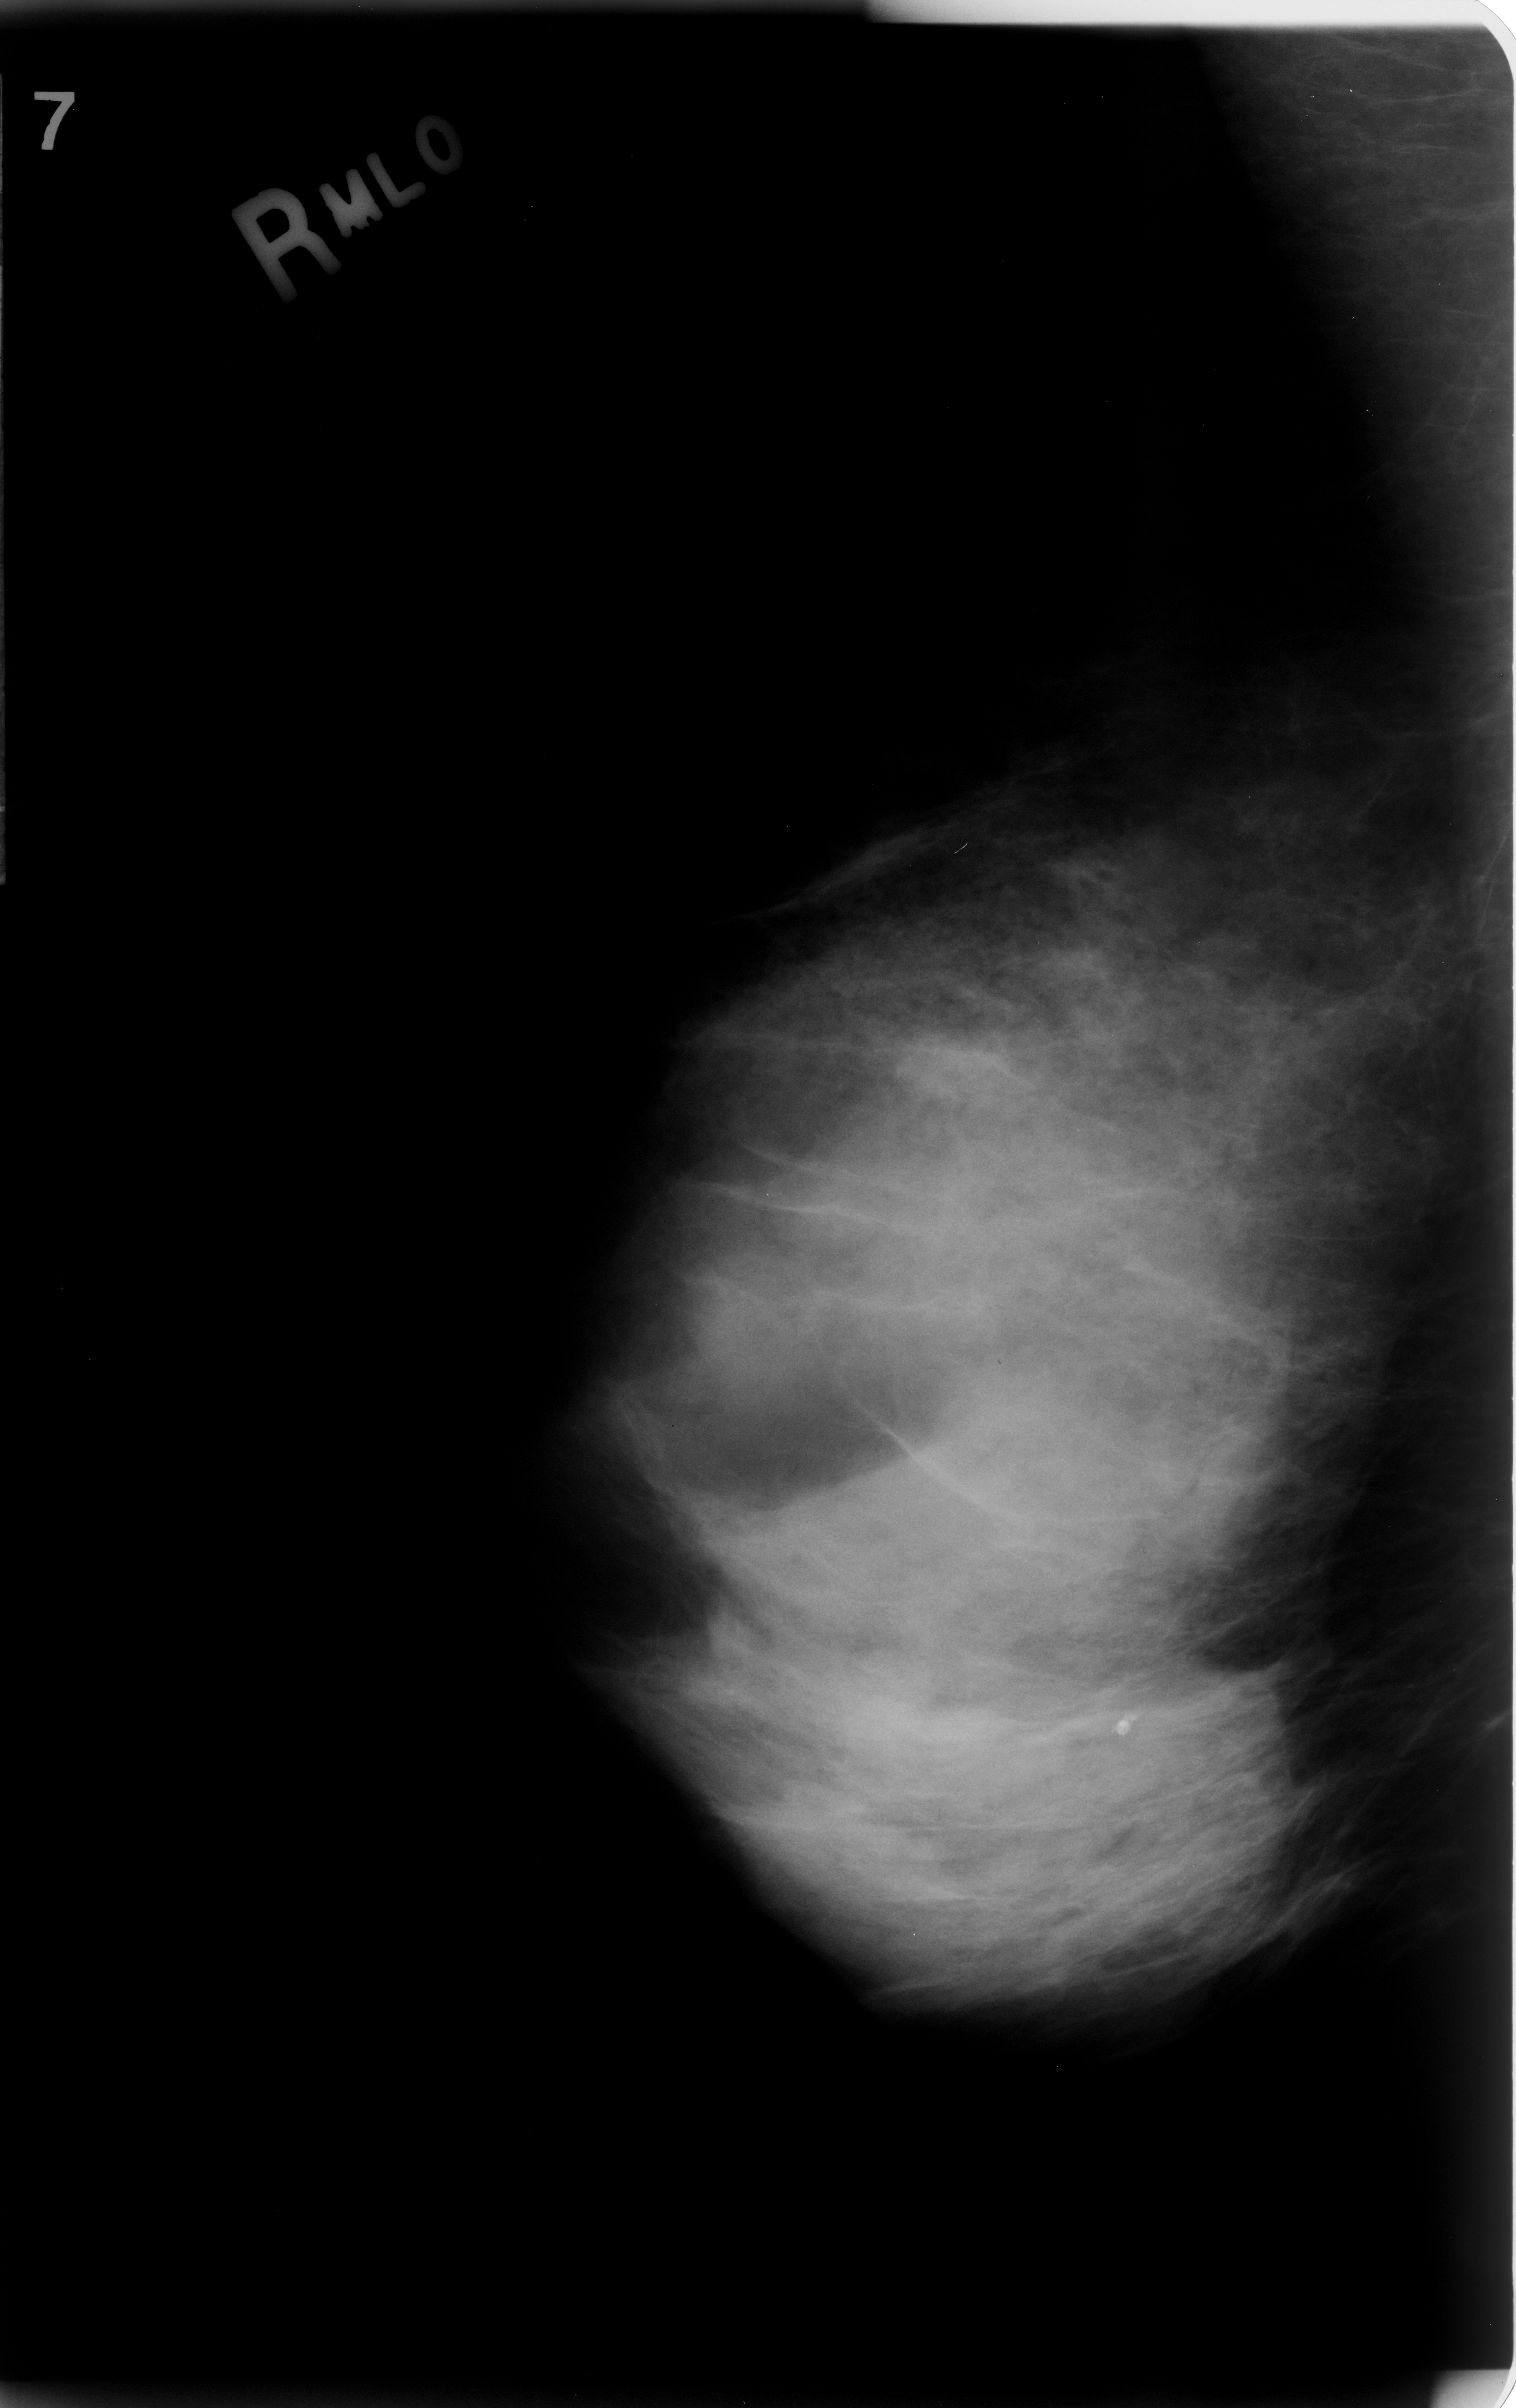
Scanned film-screen mammogram. Right breast. MLO view. BI-RADS breast density category 4 (scale 1–4). 1516 × 2408 image matrix.
Expert-marked regions of interest on this image (one box per marked abnormality):
- calcifications, morphology dystrophic, distribution clustered; BI-RADS assessment category 3; pathology (as recorded): benign: bounding box [x1, y1, x2, y2] px = [1055, 1662, 1195, 1810]